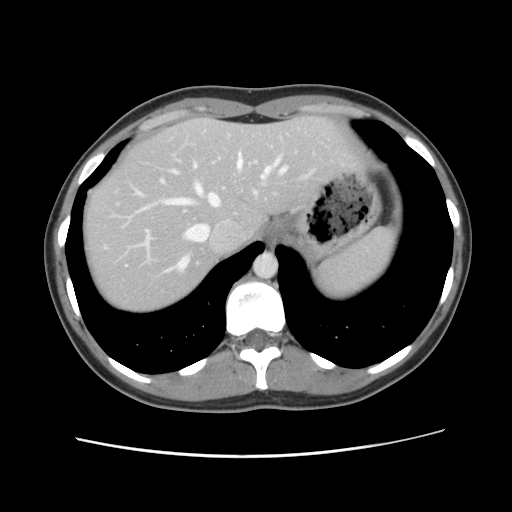
Contrast-enhanced abdominal CT, one axial slice; slice 97 of 134 in the series (ordered by position); intravenous contrast given; soft-tissue window (W 400 / L 40 HU); 512 × 512 image matrix. Female patient, age 33 years. From the clinical record (not read from this slice): diagnosis: colorectal cancer liver metastases, imaged before liver resection; multiple liver metastases: yes; largest metastasis: 4.5 cm; disease in both lobes: yes.
Annotated regions visible in this slice (outlined manually by an expert reader):
- hepatic veins: bounding box <136,152,287,270> (left, top, right, bottom; pixels)
- liver: <82,117,357,314>
- planned liver remnant (the part of the liver to remain after resection): <82,116,359,314>
- portal vein (with intrahepatic branches): <116,202,153,250>